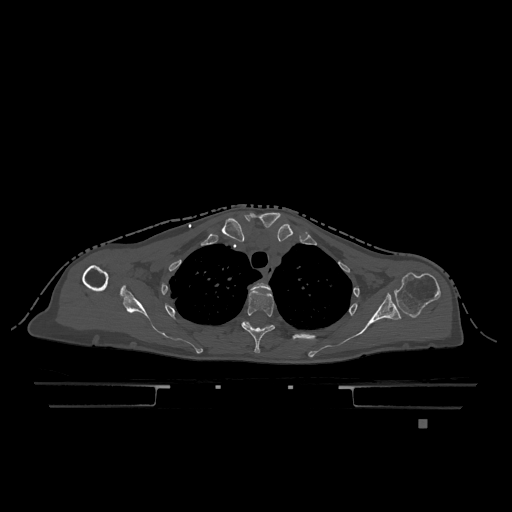
CT including the spine, one axial slice. Position 920 of 1317 along the scan axis. Bone window (W 1800 / L 400 HU). 0.5 mm slice thickness. 512 × 512 image matrix. Patient: female, 74 years. Case-level facts recorded for this patient, not image findings: primary cancer: lung; vertebrae with lytic lesions (as recorded): T1, T4, T5, T6, L4, L5.
Outlined on this slice (semi-automatic segmentation, software-assisted and operator-edited):
- T2 vertebra: bounding box [x1, y1, x2, y2] px = [250, 282, 270, 292]
- T3 vertebra: [241, 290, 275, 353]
- T4 vertebra: [244, 321, 307, 340]